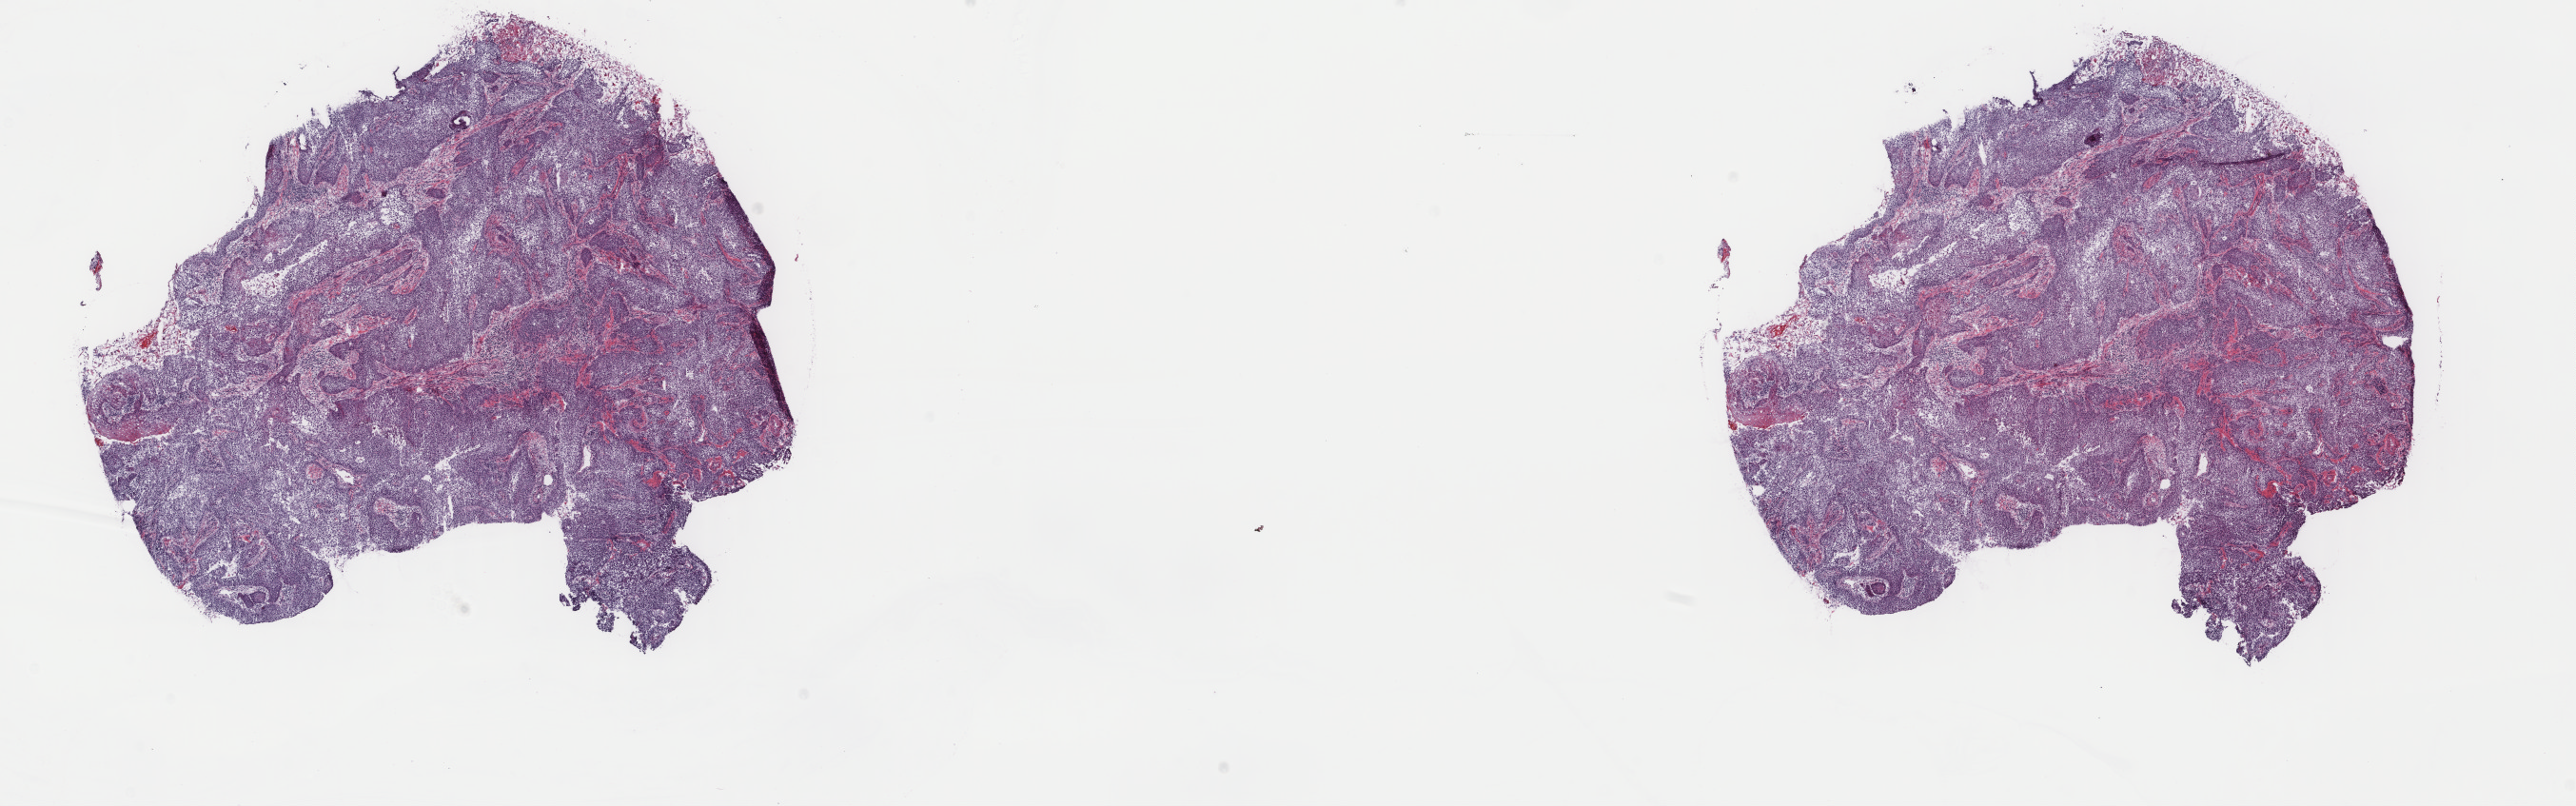
Whole-slide histology image, H&E — shown as a low-resolution overview of the whole scanned area (about 21.5 x 6.7 mm, acquisition: 40x scan), frozen section from the top of the tissue portion, sample: primary tumour, cervix. Female, age 32 years at initial diagnosis. Histologic grade: G3 (poorly differentiated). Pathologist review of this section (percent, as recorded): tumour cells 90%, tumour nuclei 90%, normal cells 0%, stromal cells 10%, necrosis 0%. Inflammatory infiltration, as recorded: lymphocyte infiltration 80%, monocyte infiltration 0%, neutrophil infiltration 20%.
FIGO stage: IIIB. Pathologic diagnosis: Squamous cell carcinoma, NOS (cervix uteri).